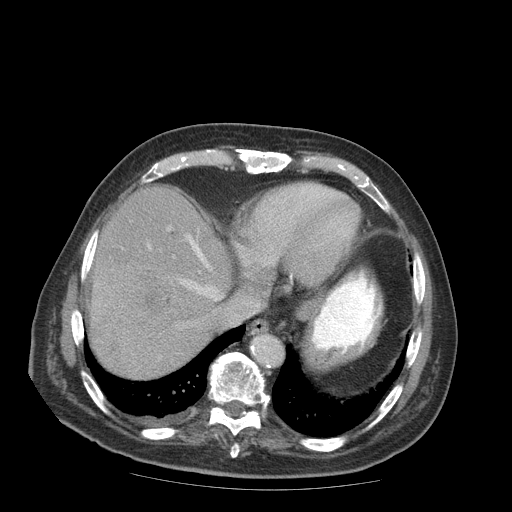
Contrast-enhanced abdominal CT (liver protocol), one axial slice; position 76 of 99 along the scan axis; reconstruction kernel STANDARD; soft-tissue window (W 400 / L 40 HU); 2.5 mm slice thickness; 512 × 512 image matrix. From the clinical record (not read from this slice): diagnosis: hepatocellular carcinoma (patient treated with transarterial chemoembolisation; whether this scan precedes or follows treatment is not stated here); TNM stage (as recorded): Stage-IIIB; Child-Pugh class: A; tumour nodularity: multinodular.
Outlined on this slice (semi-automatically segmented with operator editing):
- liver parenchyma outside the tumour (the mass and vessels are separate outlines, so this box may not span the whole liver): bounding box <90,186,230,376> (left, top, right, bottom; pixels)
- mass: <90,255,173,320>
- liver vessels: <147,228,210,296>